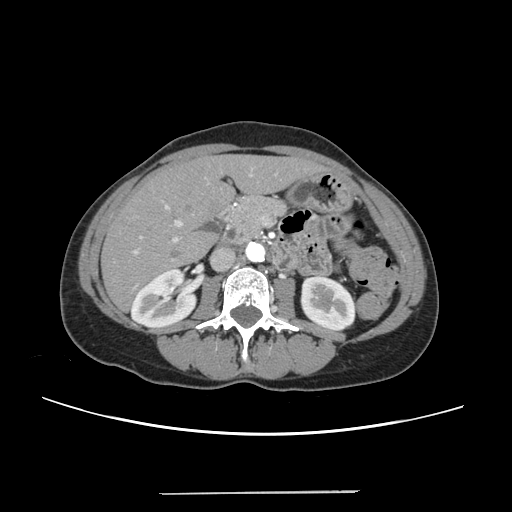
Contrast-enhanced abdominal CT, one axial slice. Slice 107 of 240 in the series (ordered by position). 120 kVp. Intravenous contrast given. Soft-tissue window (W 400 / L 40 HU). 1.25 mm slice thickness. 512 × 512 image matrix. Female patient, age 60 years. Case-level facts recorded for this patient, not image findings: diagnosis: colorectal cancer liver metastases, imaged before liver resection; multiple liver metastases: no; largest metastasis: 1.5 cm; disease in both lobes: no.
Structures marked on this image (expert manual segmentation):
- liver: bounding box <104,157,319,308> (left, top, right, bottom; pixels)
- planned liver remnant (the part of the liver to remain after resection): <104,157,319,308>
- portal vein (with intrahepatic branches): <132,173,252,255>